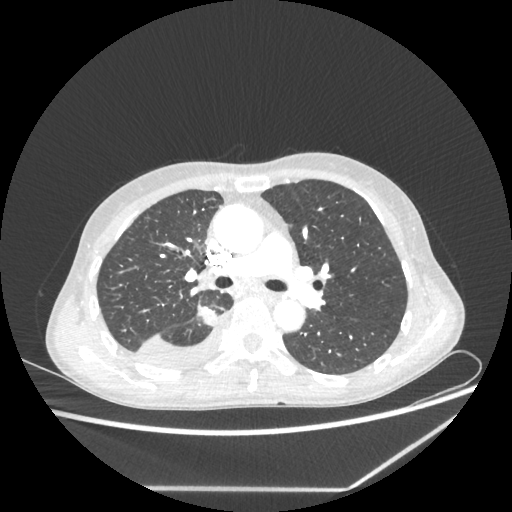
Chest CT, one axial slice. Slice 143 of 237 in the series (ordered by position). Reconstruction kernel STANDARD. 80 kVp. Lung window (W 1500 / L -600 HU). 1.25 mm slice thickness. 512 × 512 image matrix. Patient: female, 59 years. Case-level facts recorded for this patient, not image findings: clinical TNM (as recorded): T1c N1 M1.
Structures marked on this image (rectangle marked by the reading radiologist):
- lung tumour (recorded histology: adenocarcinoma): bounding box <195,305,221,329> (left, top, right, bottom; pixels)